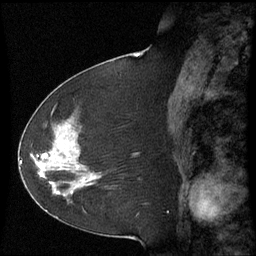
Breast MRI (dynamic contrast-enhanced), one sagittal slice; position 28 of 60 along the scan axis; dynamic contrast-enhanced series, image 2 of 3 at this slice position (ordered by acquisition); 1.5 T; TE 4.2 ms, TR 8.9 ms; 2.3 mm slice thickness; 256 × 256 image matrix, field of view 210 × 210 mm. Female patient, age 51 years. Case-level facts recorded for this patient, not image findings: setting: breast cancer imaged before/during neoadjuvant chemotherapy; receptor status: HR-positive, HER2-negative.
Outlined on this slice (semi-automatic segmentation, software-assisted and operator-edited):
- analysis volume of interest (the breast-tissue region the enhancement analysis was run in; not a lesion): bounding box <50,118,102,187> (left, top, right, bottom; pixels)
- tumour enhancement mask (voxels above the 70 % enhancement threshold inside the analysis volume of interest): <50,158,52,160>